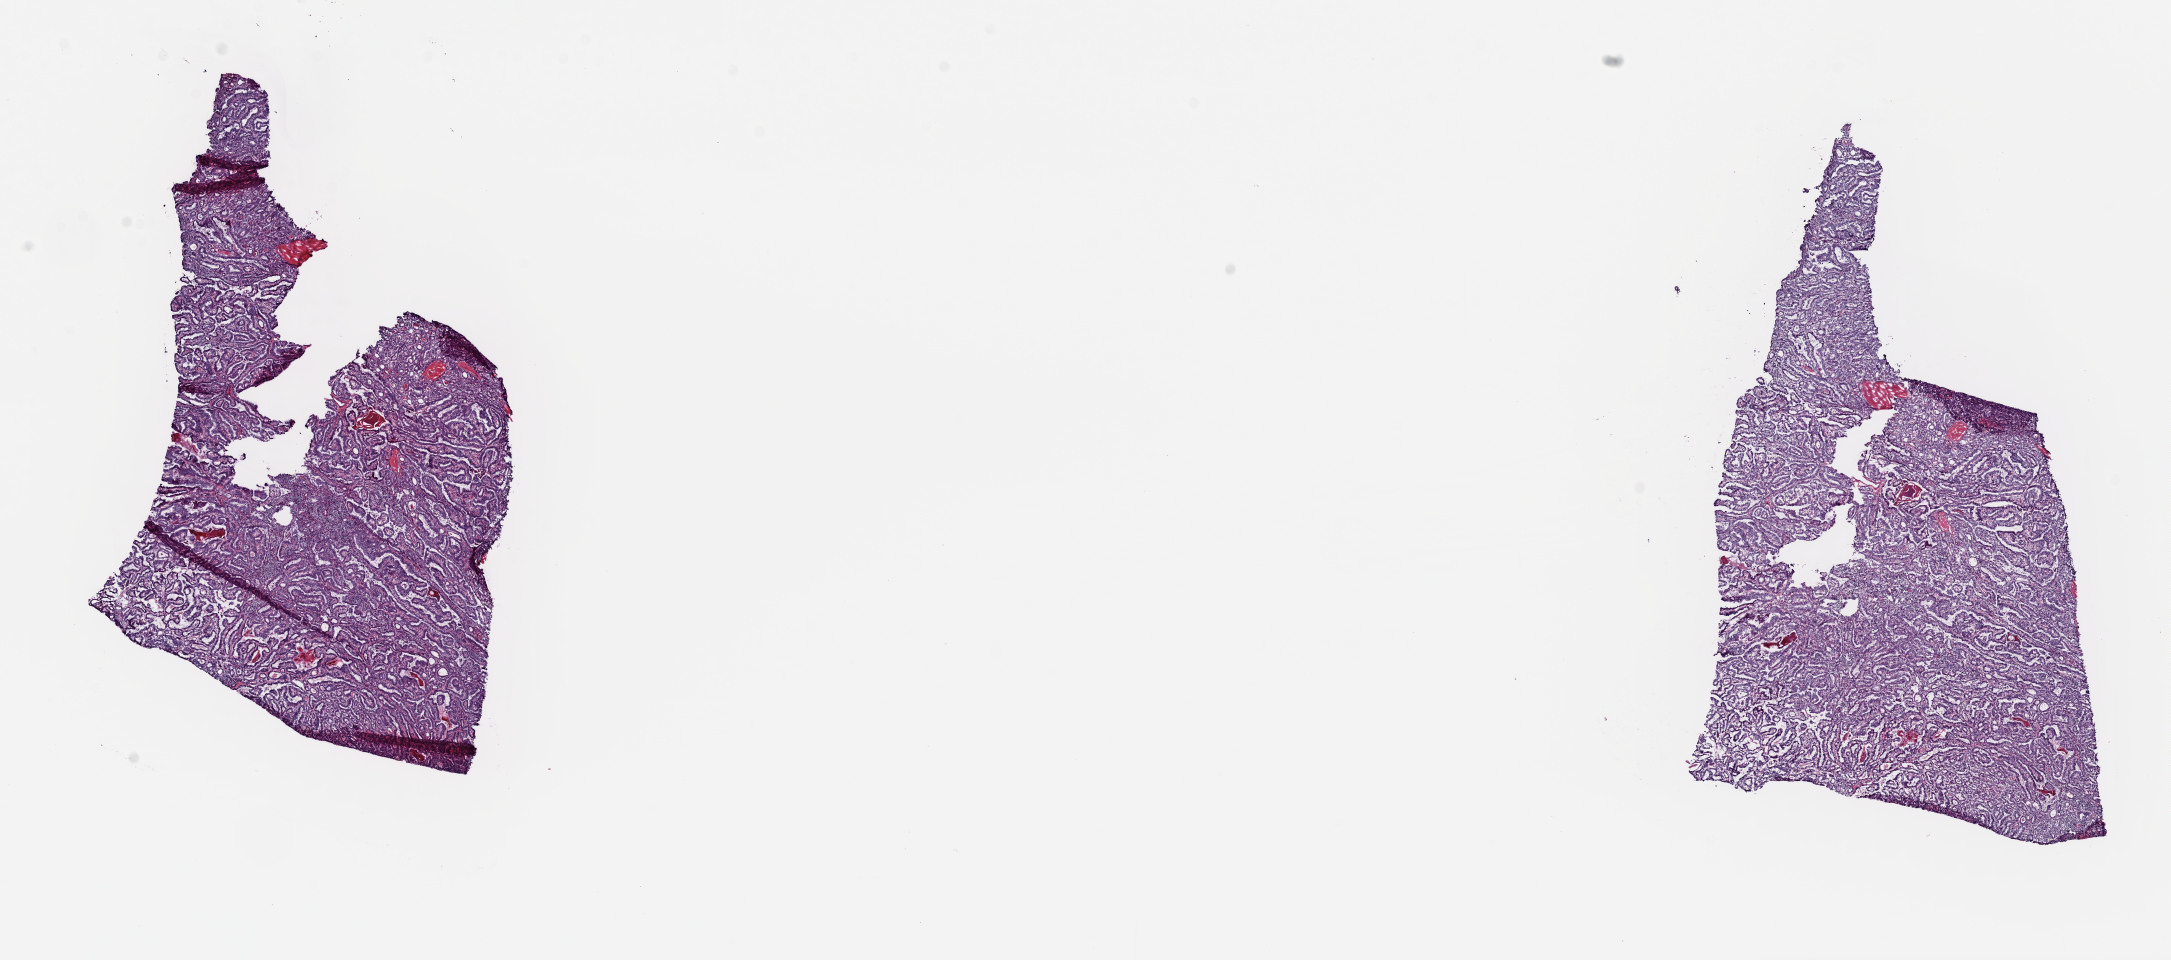
Hematoxylin and eosin (H&E) stained whole-slide image — a low-resolution overview of the entire scanned area, about 17.2 x 7.6 mm (acquisition: 40x scan), frozen section from the top of the tissue portion, thyroid, primary tumour sample. Male, age 42 years at initial diagnosis. Composition of this section per pathologist review: tumour cells 90%, tumour nuclei 90%.
Diagnosis: Papillary adenocarcinoma, NOS.